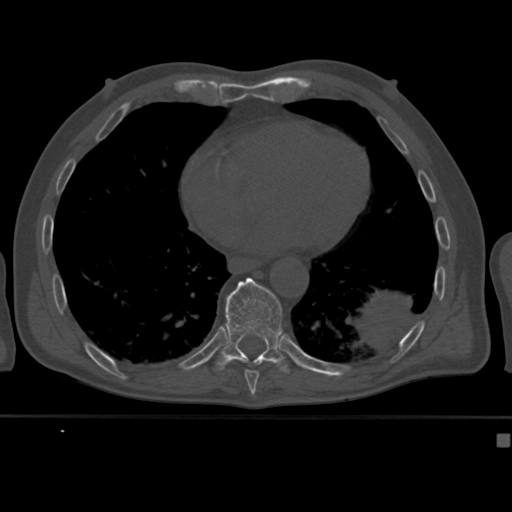
CT including the spine, one axial slice; slice 235 of 430 in the series (ordered by position); bone window (W 1800 / L 400 HU); 1.5 mm slice thickness; 512 × 512 image matrix, field of view 337 × 337 mm. Patient: male, 64 years. From the clinical record (not read from this slice): primary cancer: uterus.
Outlined on this slice (semi-automatically segmented with operator editing):
- T10 vertebra: bounding box (x1, y1, x2, y2) in pixels: (216, 277, 289, 374)
- T9 vertebra: (244, 369, 259, 382)